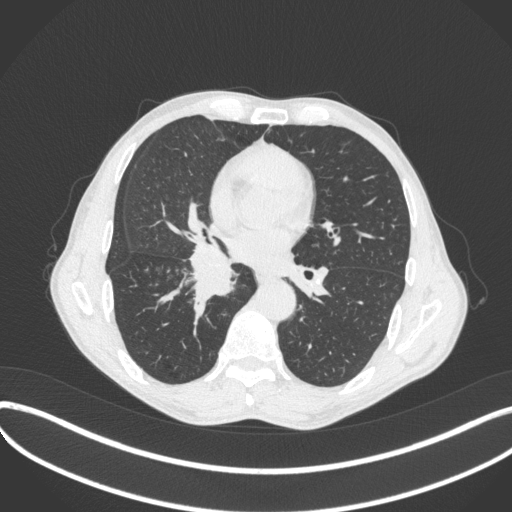
Chest CT, one axial slice; position 211 of 481 along the scan axis; reconstruction kernel B31f; 120 kVp; lung window (W 1500 / L -600 HU); 512 × 512 image matrix. Male patient, age 65 years. Case-level facts recorded for this patient, not image findings: clinical TNM (as recorded): T2a N0 M0; histopathological grade: G2.
Annotated regions visible in this slice (bounding box drawn by a radiologist):
- lung tumour (recorded histology: squamous cell carcinoma): bounding box [x1, y1, x2, y2] px = [184, 244, 245, 304]